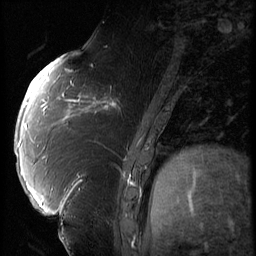
Breast MRI (dynamic contrast-enhanced), one sagittal slice; position 26 of 66 along the scan axis; 3 images stored at this slice position (order not interpretable as contrast timing); 1.5 T; TE 4.2 ms, TR 9 ms; 2.5 mm slice thickness; 256 × 256 image matrix, field of view 180 × 180 mm. Patient: female, 57 years. Case-level facts recorded for this patient, not image findings: setting: breast cancer imaged before/during neoadjuvant chemotherapy; receptor status: triple-negative.
Outlined on this slice (semi-automatically segmented with operator editing):
- analysis volume of interest (the breast-tissue region the enhancement analysis was run in; not a lesion): box from (x=86, y=74) to (x=138, y=129) px
- tumour enhancement mask (voxels above the 140 % enhancement threshold inside the analysis volume of interest): (x=86, y=87)–(x=120, y=113)